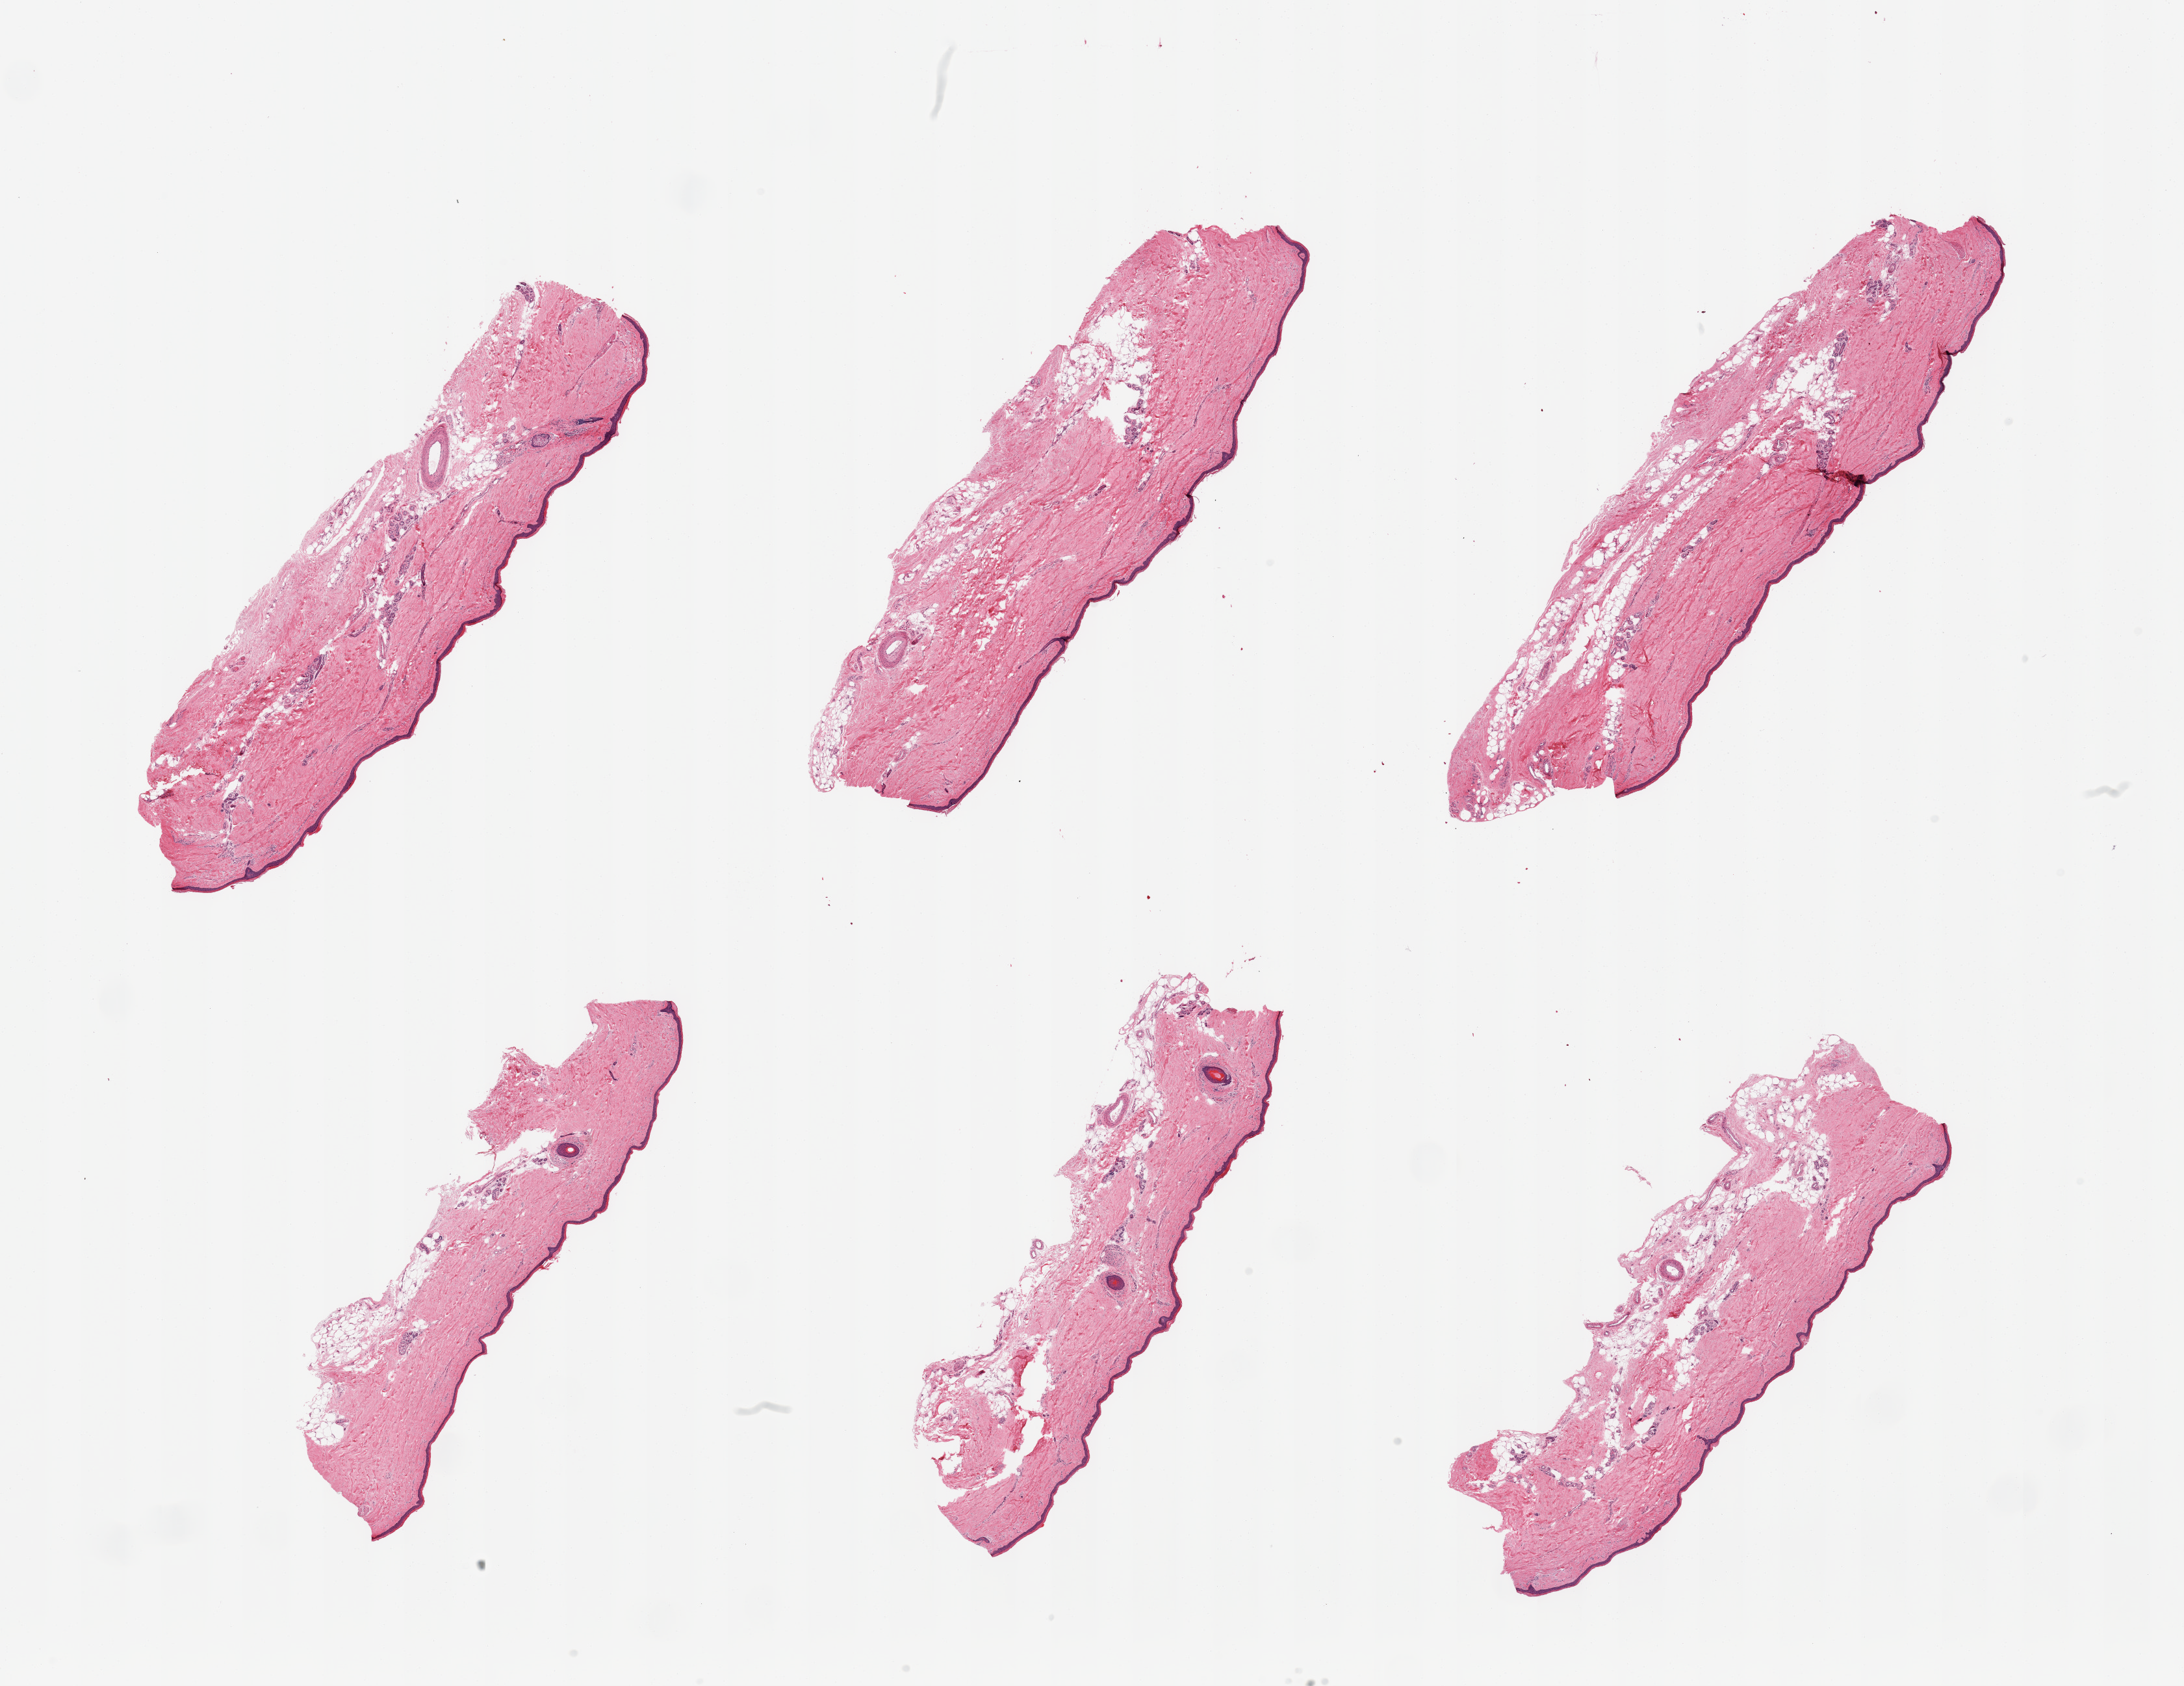
Whole-slide image, H&E stain, low-resolution overview of the scanned area, about 26.6 x 20.5 mm. PAXgene-fixed paraffin-embedded (PFPE) section. Section of skin of lower leg (target tissue). Donor tissue sample. Donor: male.
Review note (as recorded): 6 pieces; well trimmed; up to 20% dermal fat.